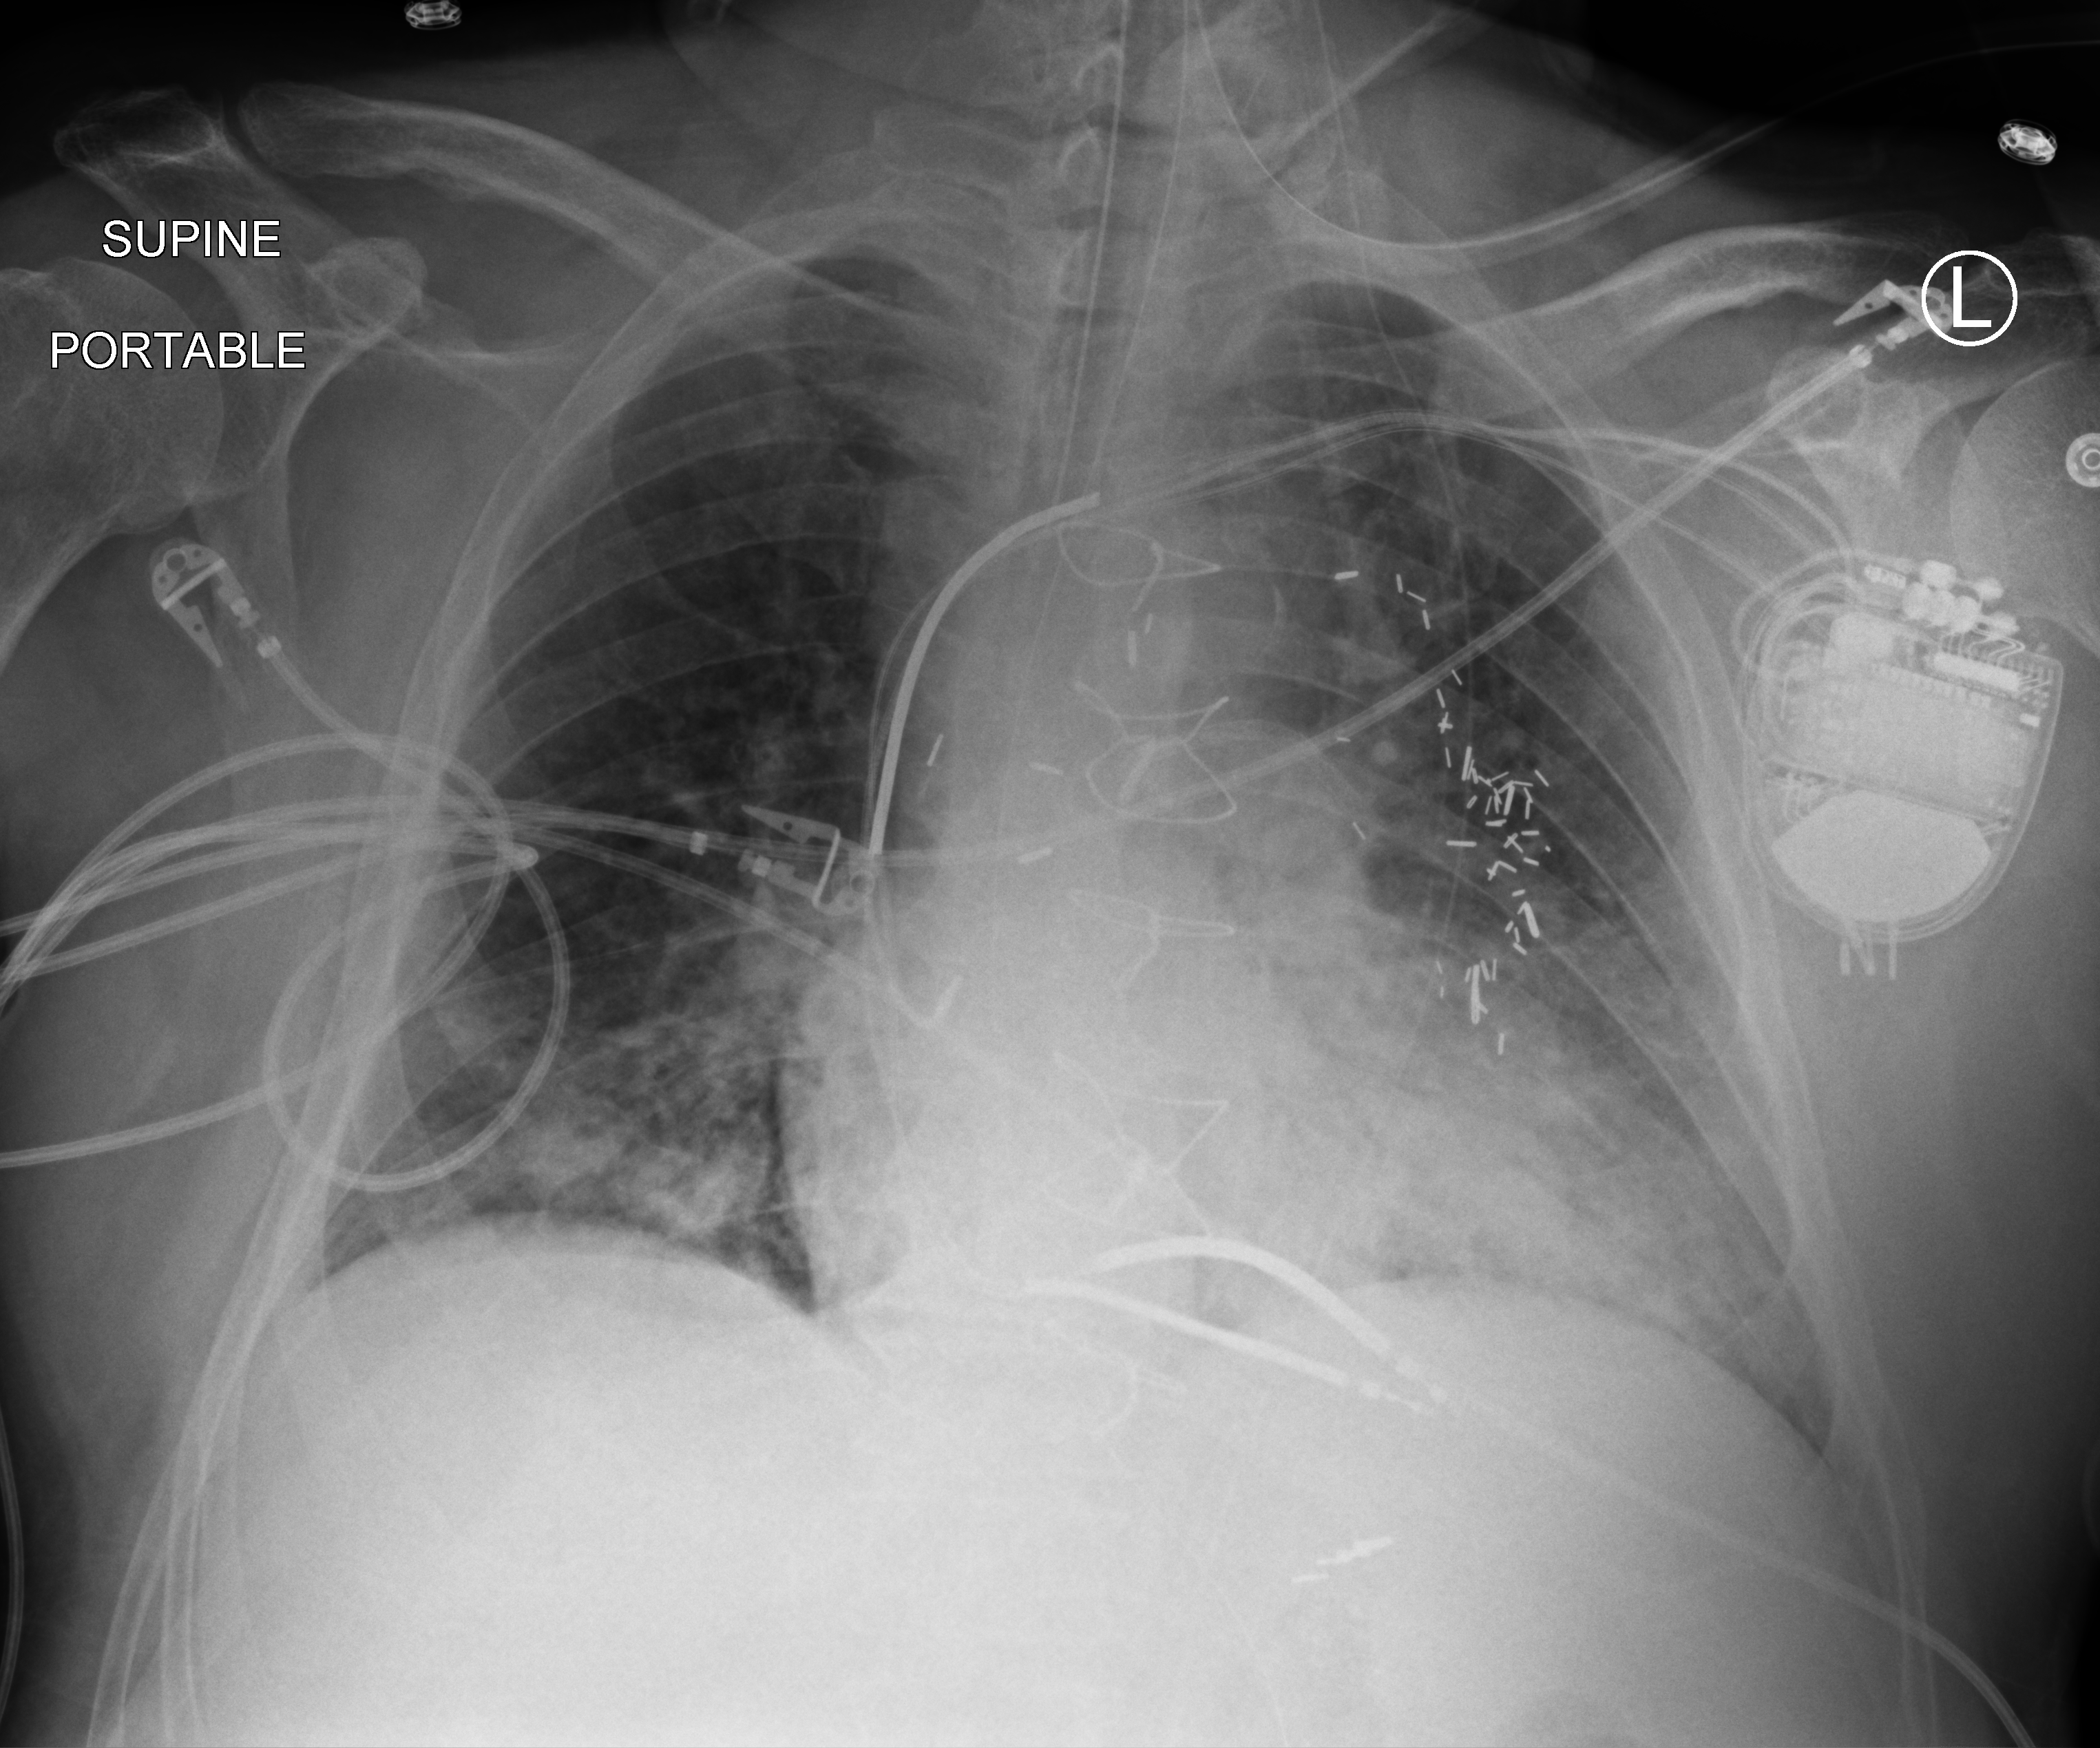
Bedside chest radiograph (computed radiography). Male patient hospitalised with COVID-19, age 60–74 years.
Admission-level facts for this patient (not findings on this image; timing relative to this image not recorded):
- mechanically ventilated during this hospital stay: yes
- COPD (admission record): no